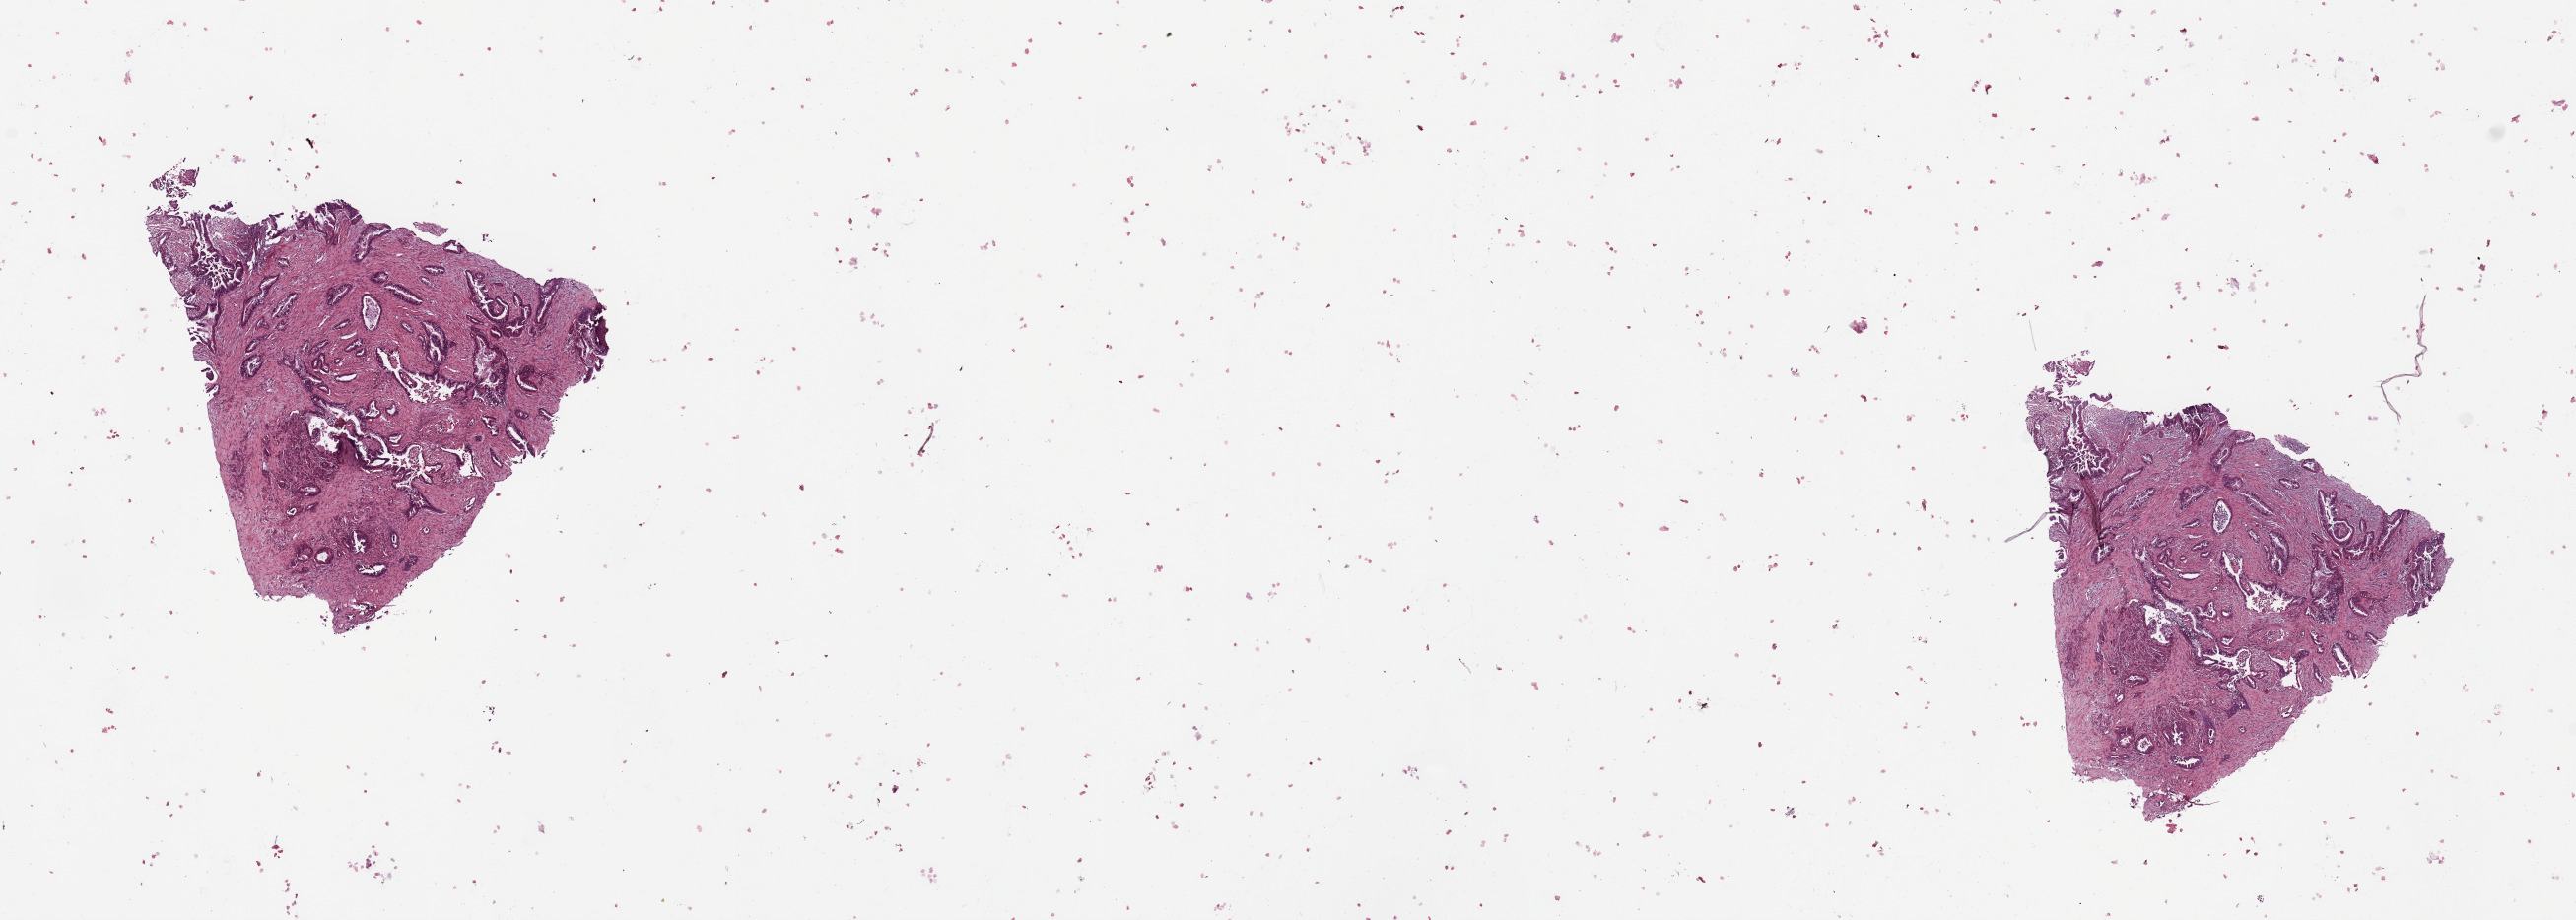
H&E-stained whole-slide image, whole scanned area (about 20.7 x 7.4 mm) shown as a low-resolution overview, tumour tissue sample, pancreas. 60-year-old female patient. Histologic grade: G2 (moderately differentiated).
- AJCC pathologic stage: IIB
- primary tumour site (as recorded): head
- histologic diagnosis: Infiltrating duct carcinoma, NOS